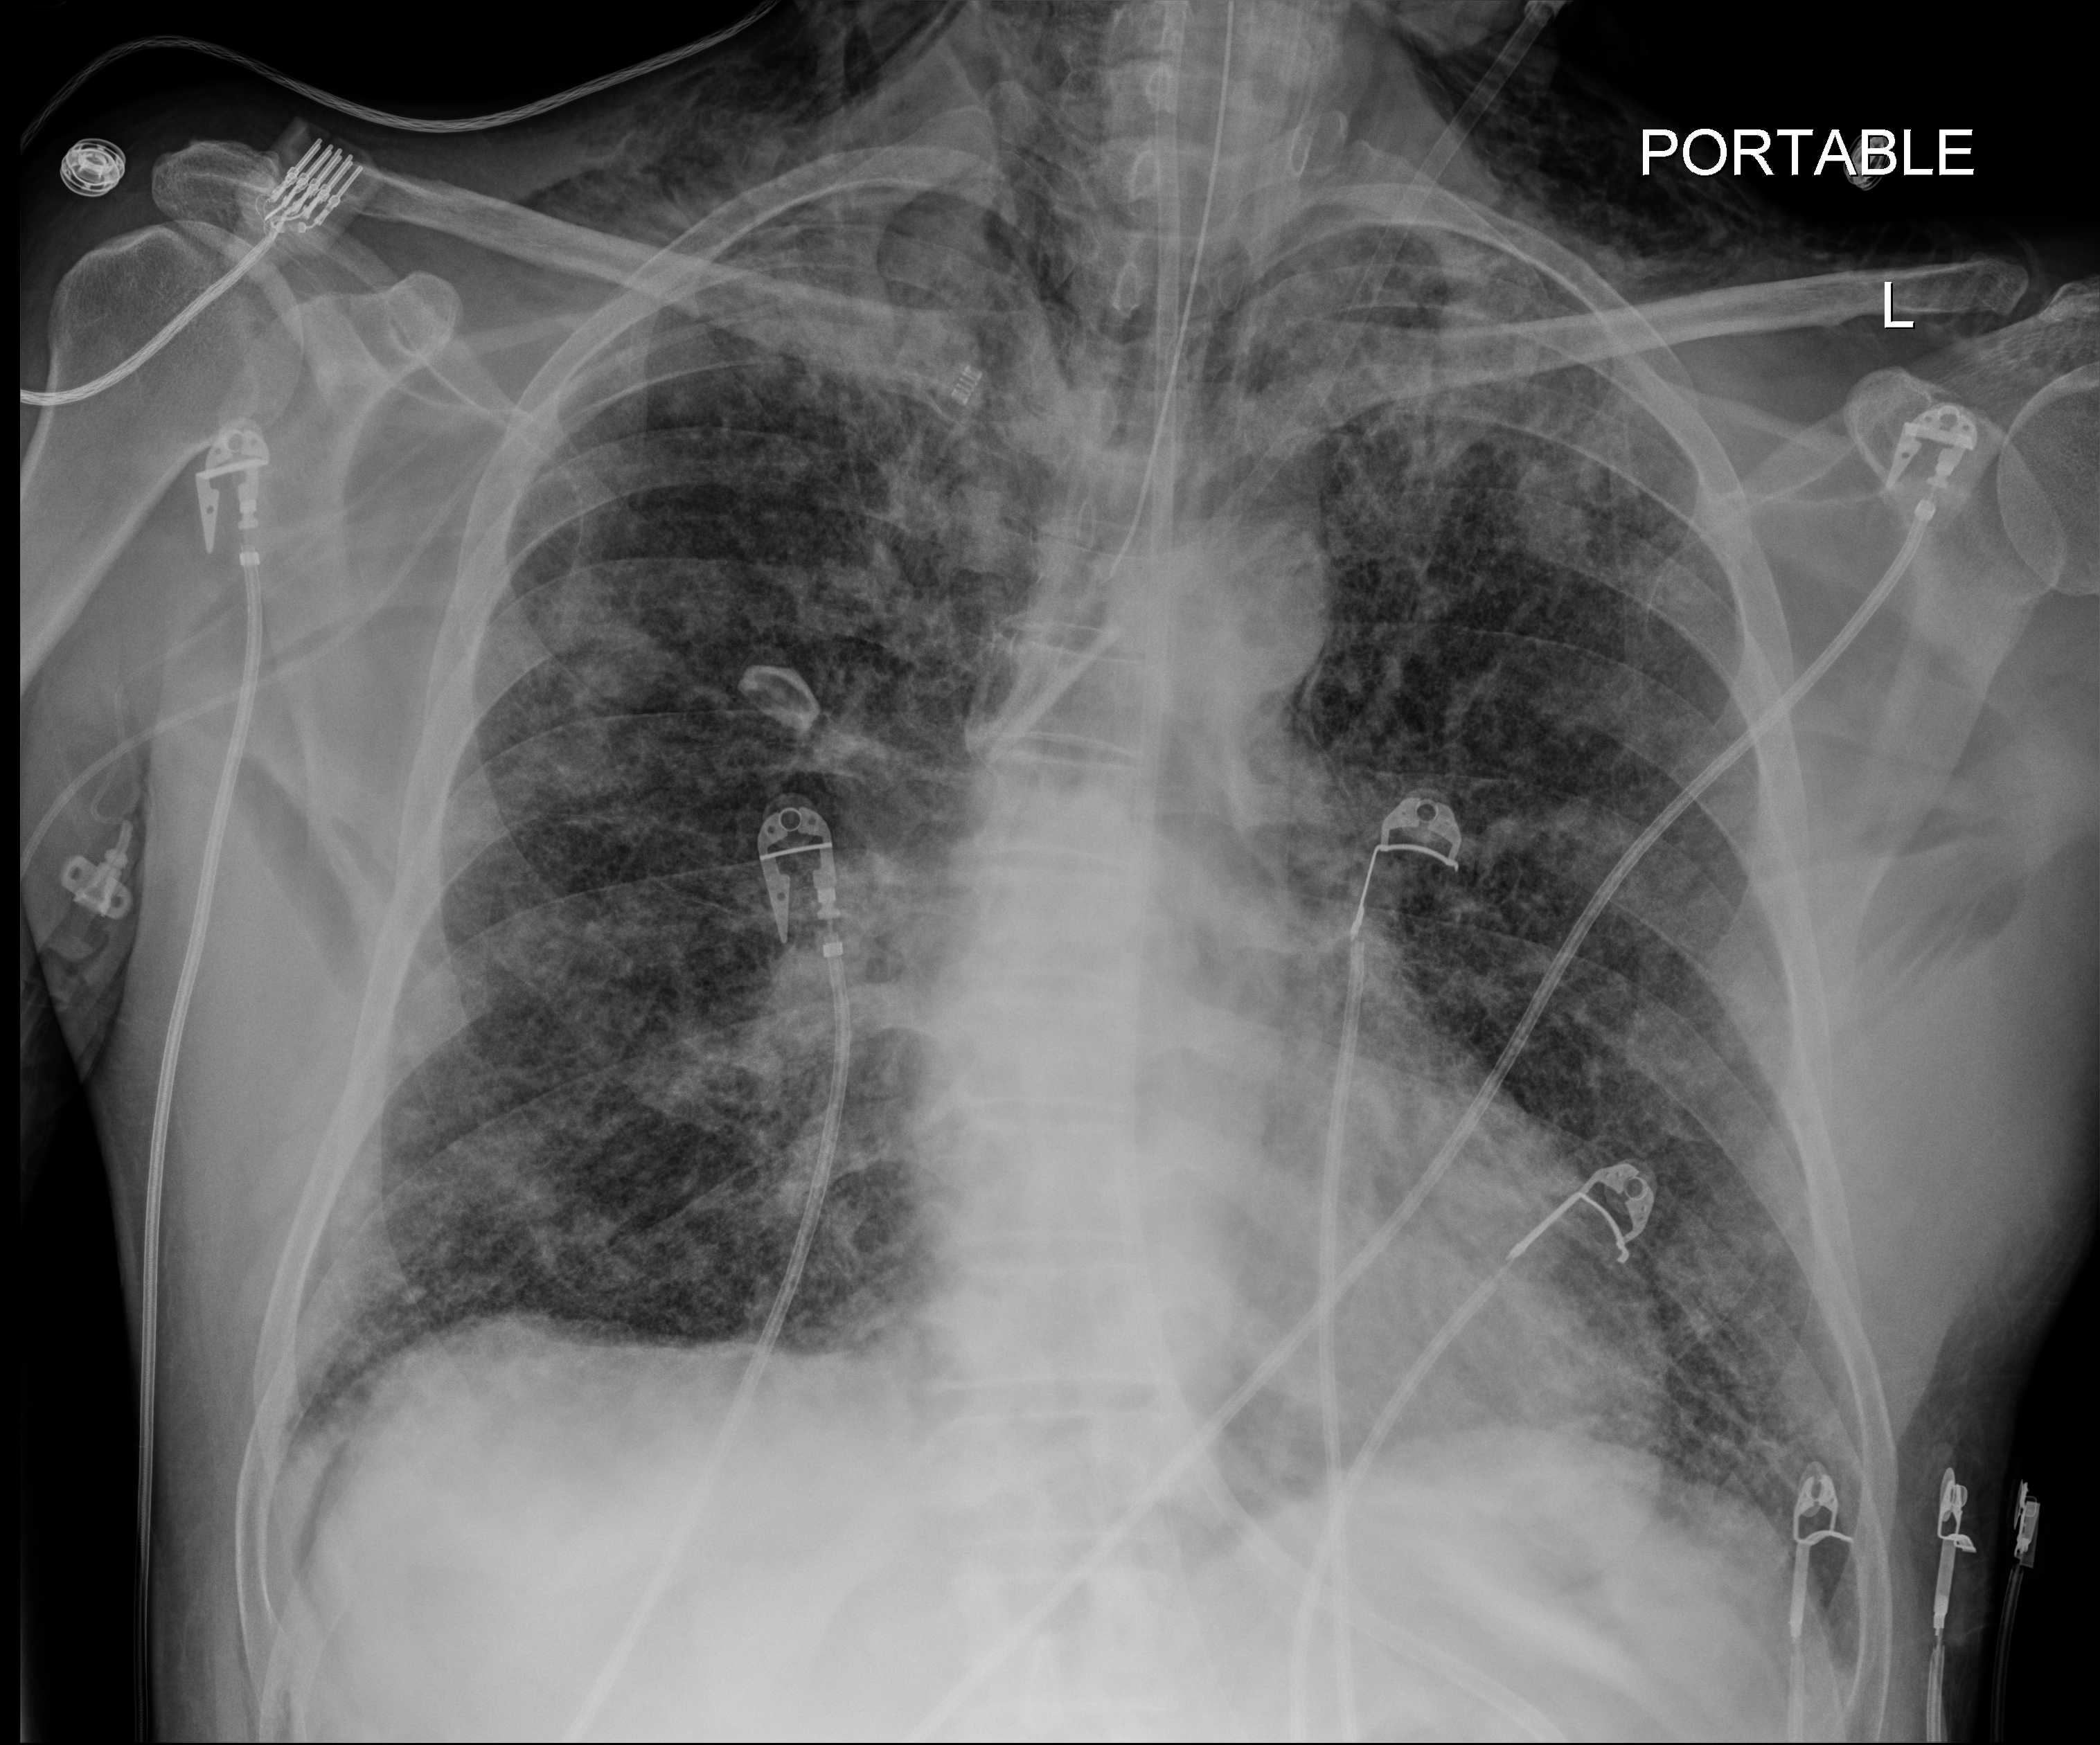
Bedside chest radiograph (digital radiography), anteroposterior (AP) projection. Male patient hospitalised with COVID-19, age 18–59 years.
Admission-level facts for this patient (not findings on this image; timing relative to this image not recorded): admitted to intensive care during this hospital stay: yes; mechanically ventilated during this hospital stay: yes; hypertension (admission record): no.